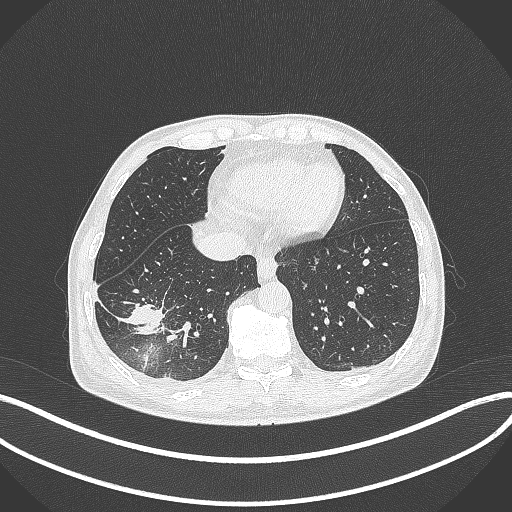
Chest CT, one axial slice; 120 kVp; lung window (W 1500 / L -600 HU); 512 × 512 image matrix. Patient: male, 64 years. Case-level facts recorded for this patient, not image findings: clinical TNM (as recorded): T3 N0 M0; histopathological grade: G2-3.
Outlined on this slice (bounding box drawn by a radiologist):
- lung tumour (recorded histology: adenocarcinoma): box from (x=119, y=296) to (x=164, y=341) px